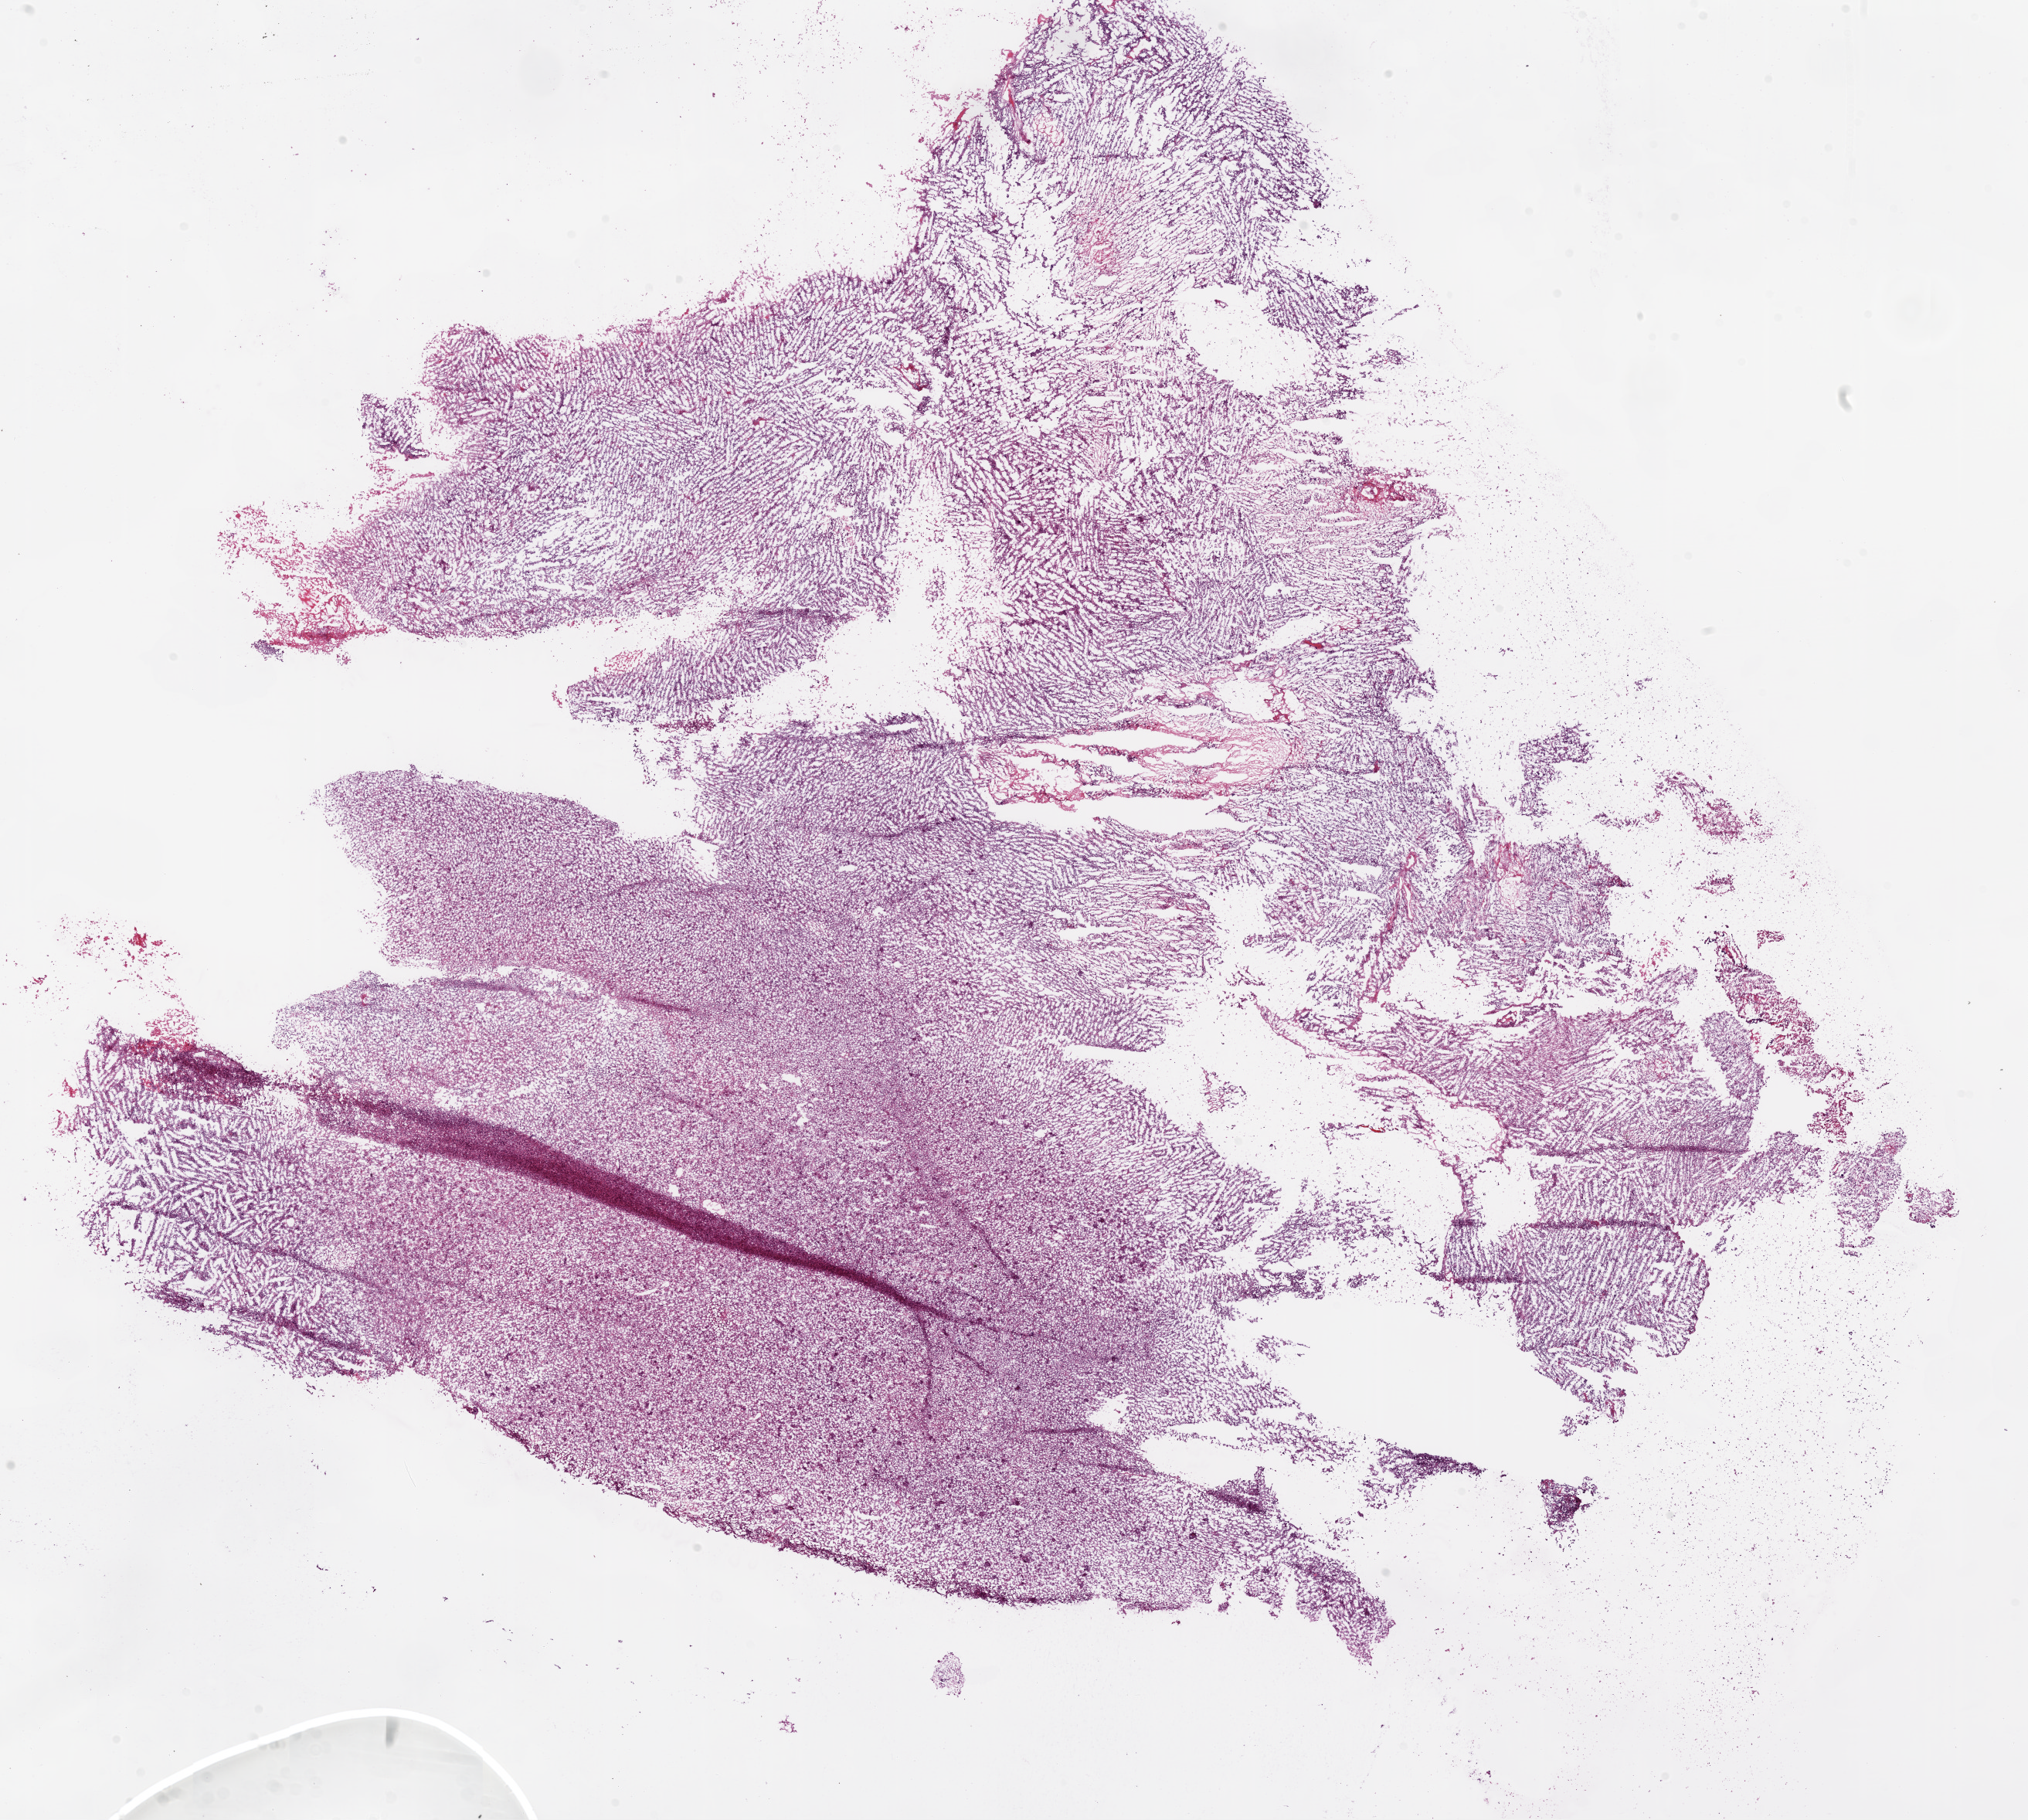
H&E whole-slide image, shown as a low-resolution overview of the whole scanned area (about 21.1 x 18.9 mm). Frozen section from the top of the tissue portion. Sample: primary tumour, brain. Male patient; age at initial diagnosis 53 years. Slide review estimates, as recorded: tumour cells 100%, tumour nuclei 80%, normal cells 0%, stromal cells 0%, necrosis 0%.
- diagnosis: Glioblastoma